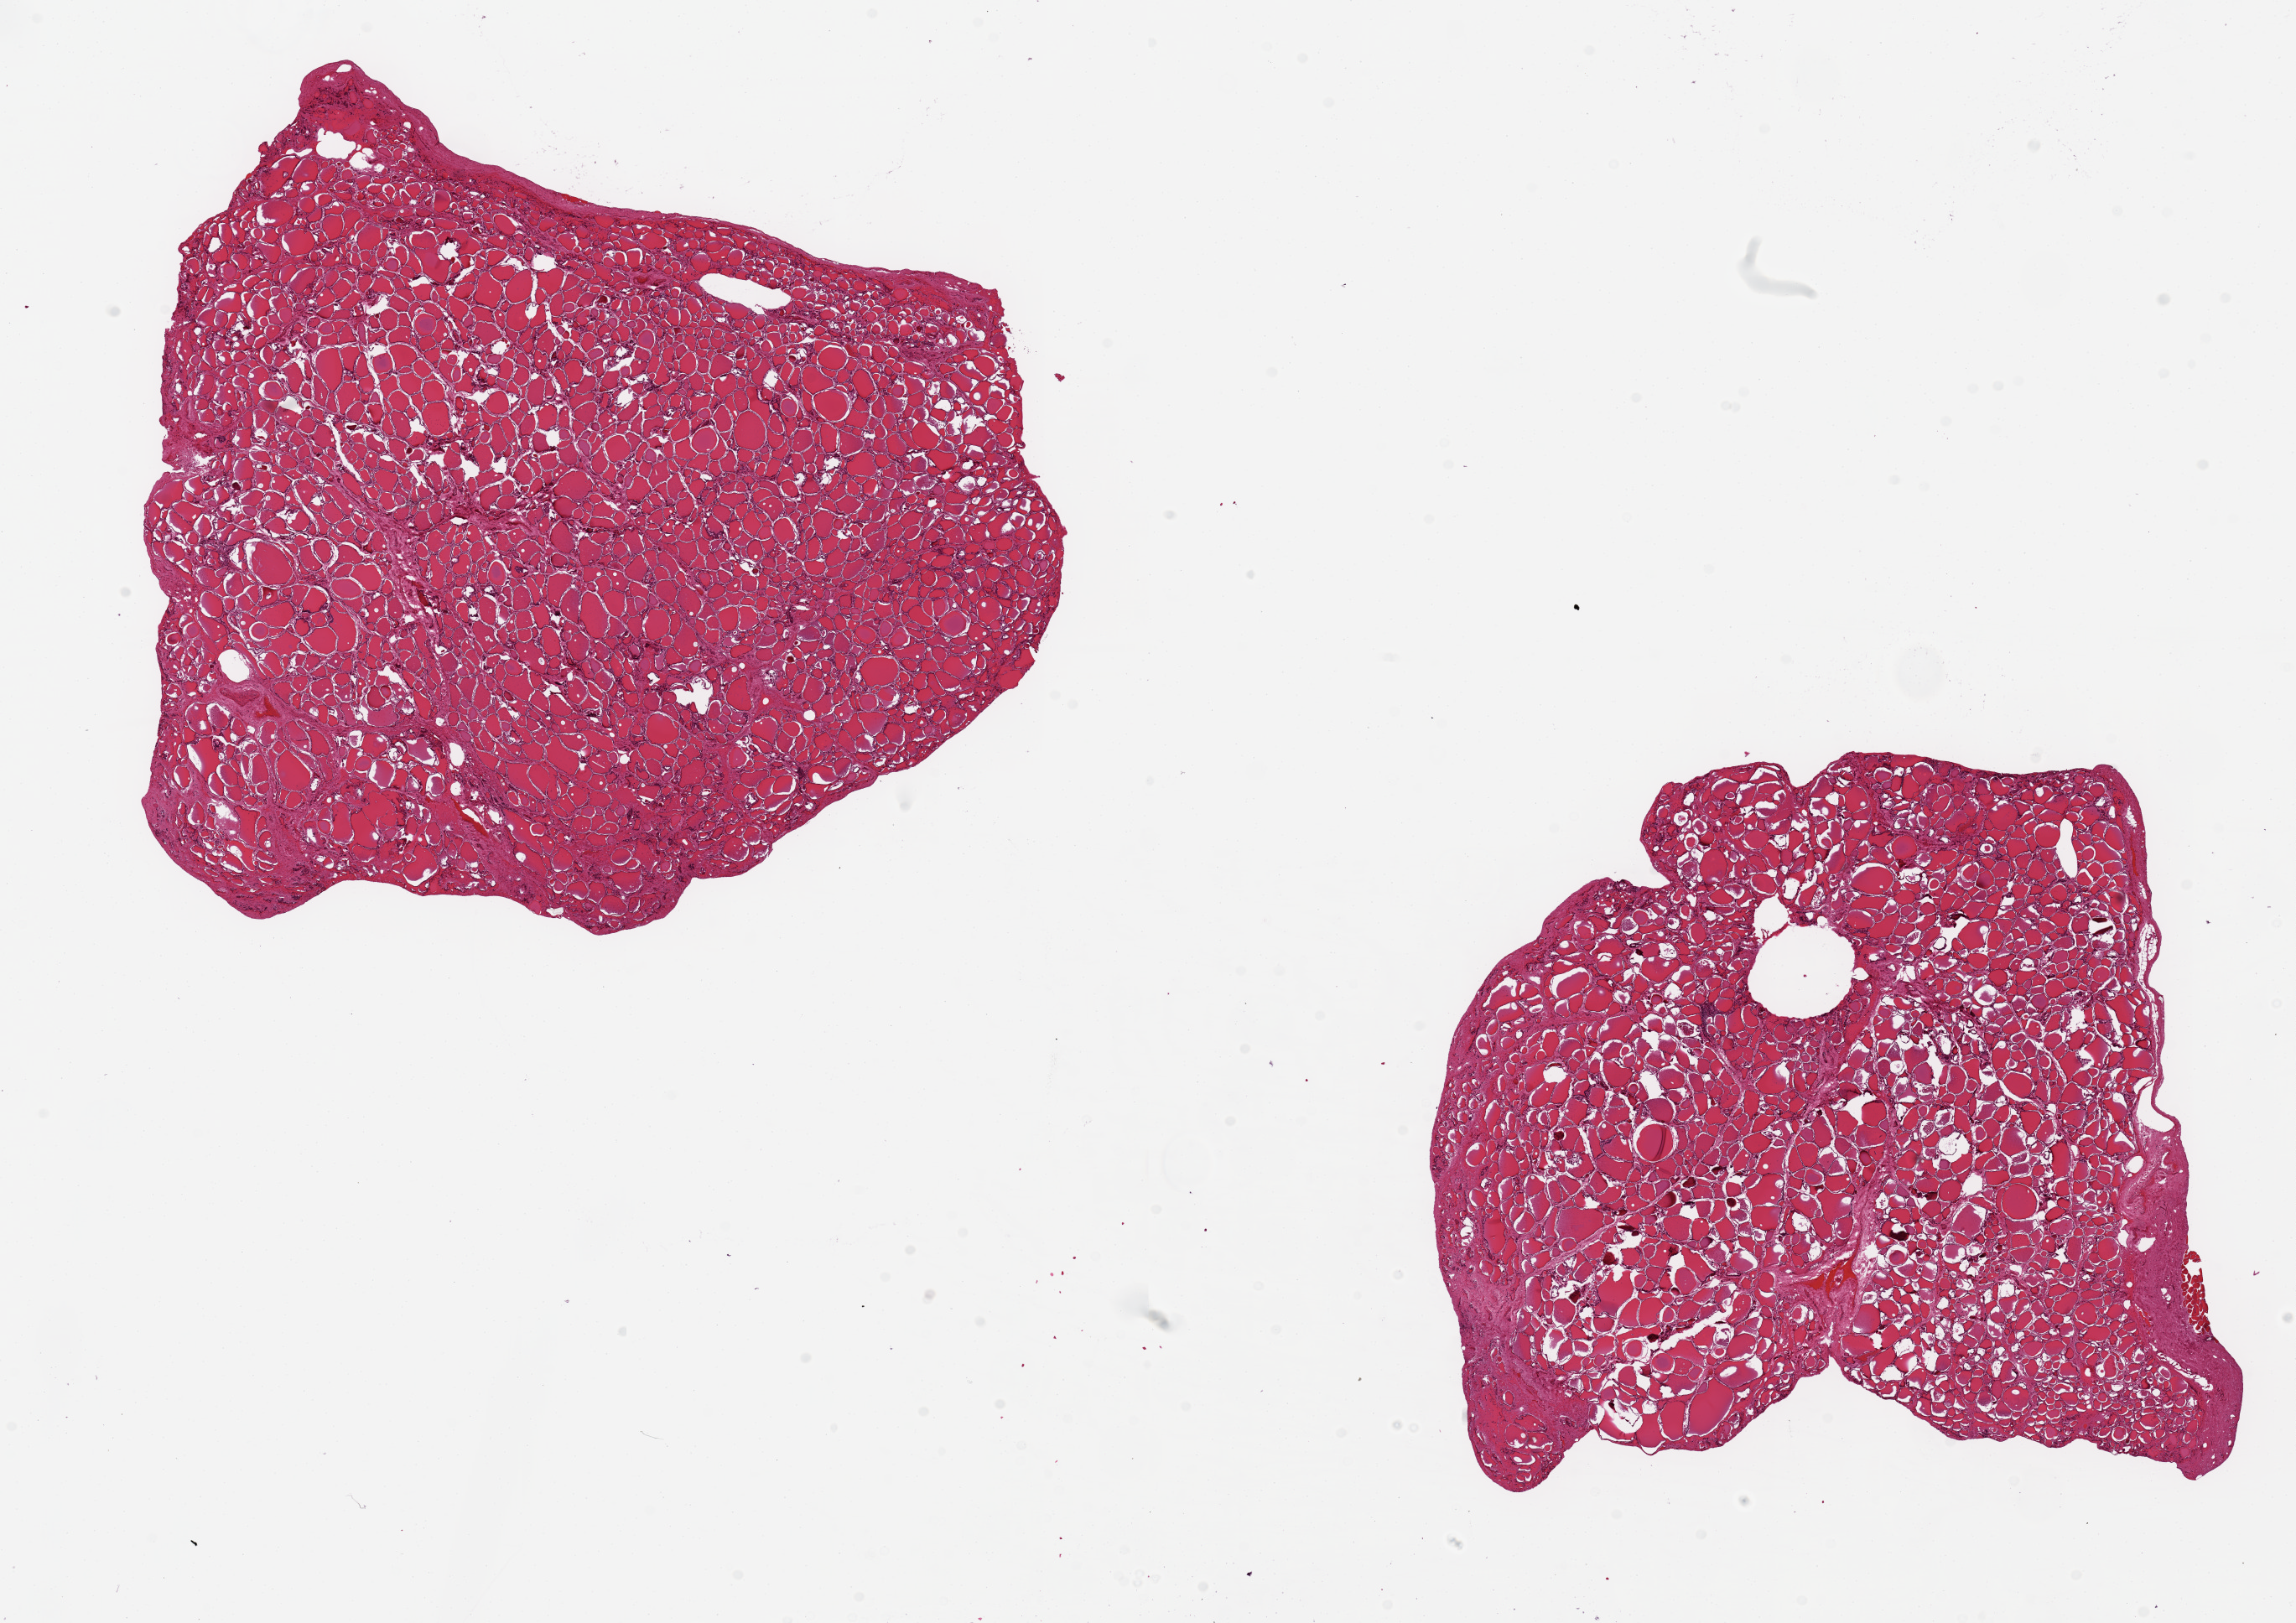
Whole-slide image, hematoxylin and eosin (H&E) stain — low-resolution overview of the scanned area, about 21.7 x 15.3 mm, PAXgene-fixed, paraffin-embedded tissue, section of thyroid (target tissue), donor tissue sample. Male donor.
Review note (as recorded): 2 aliquots, ~7x7mm.